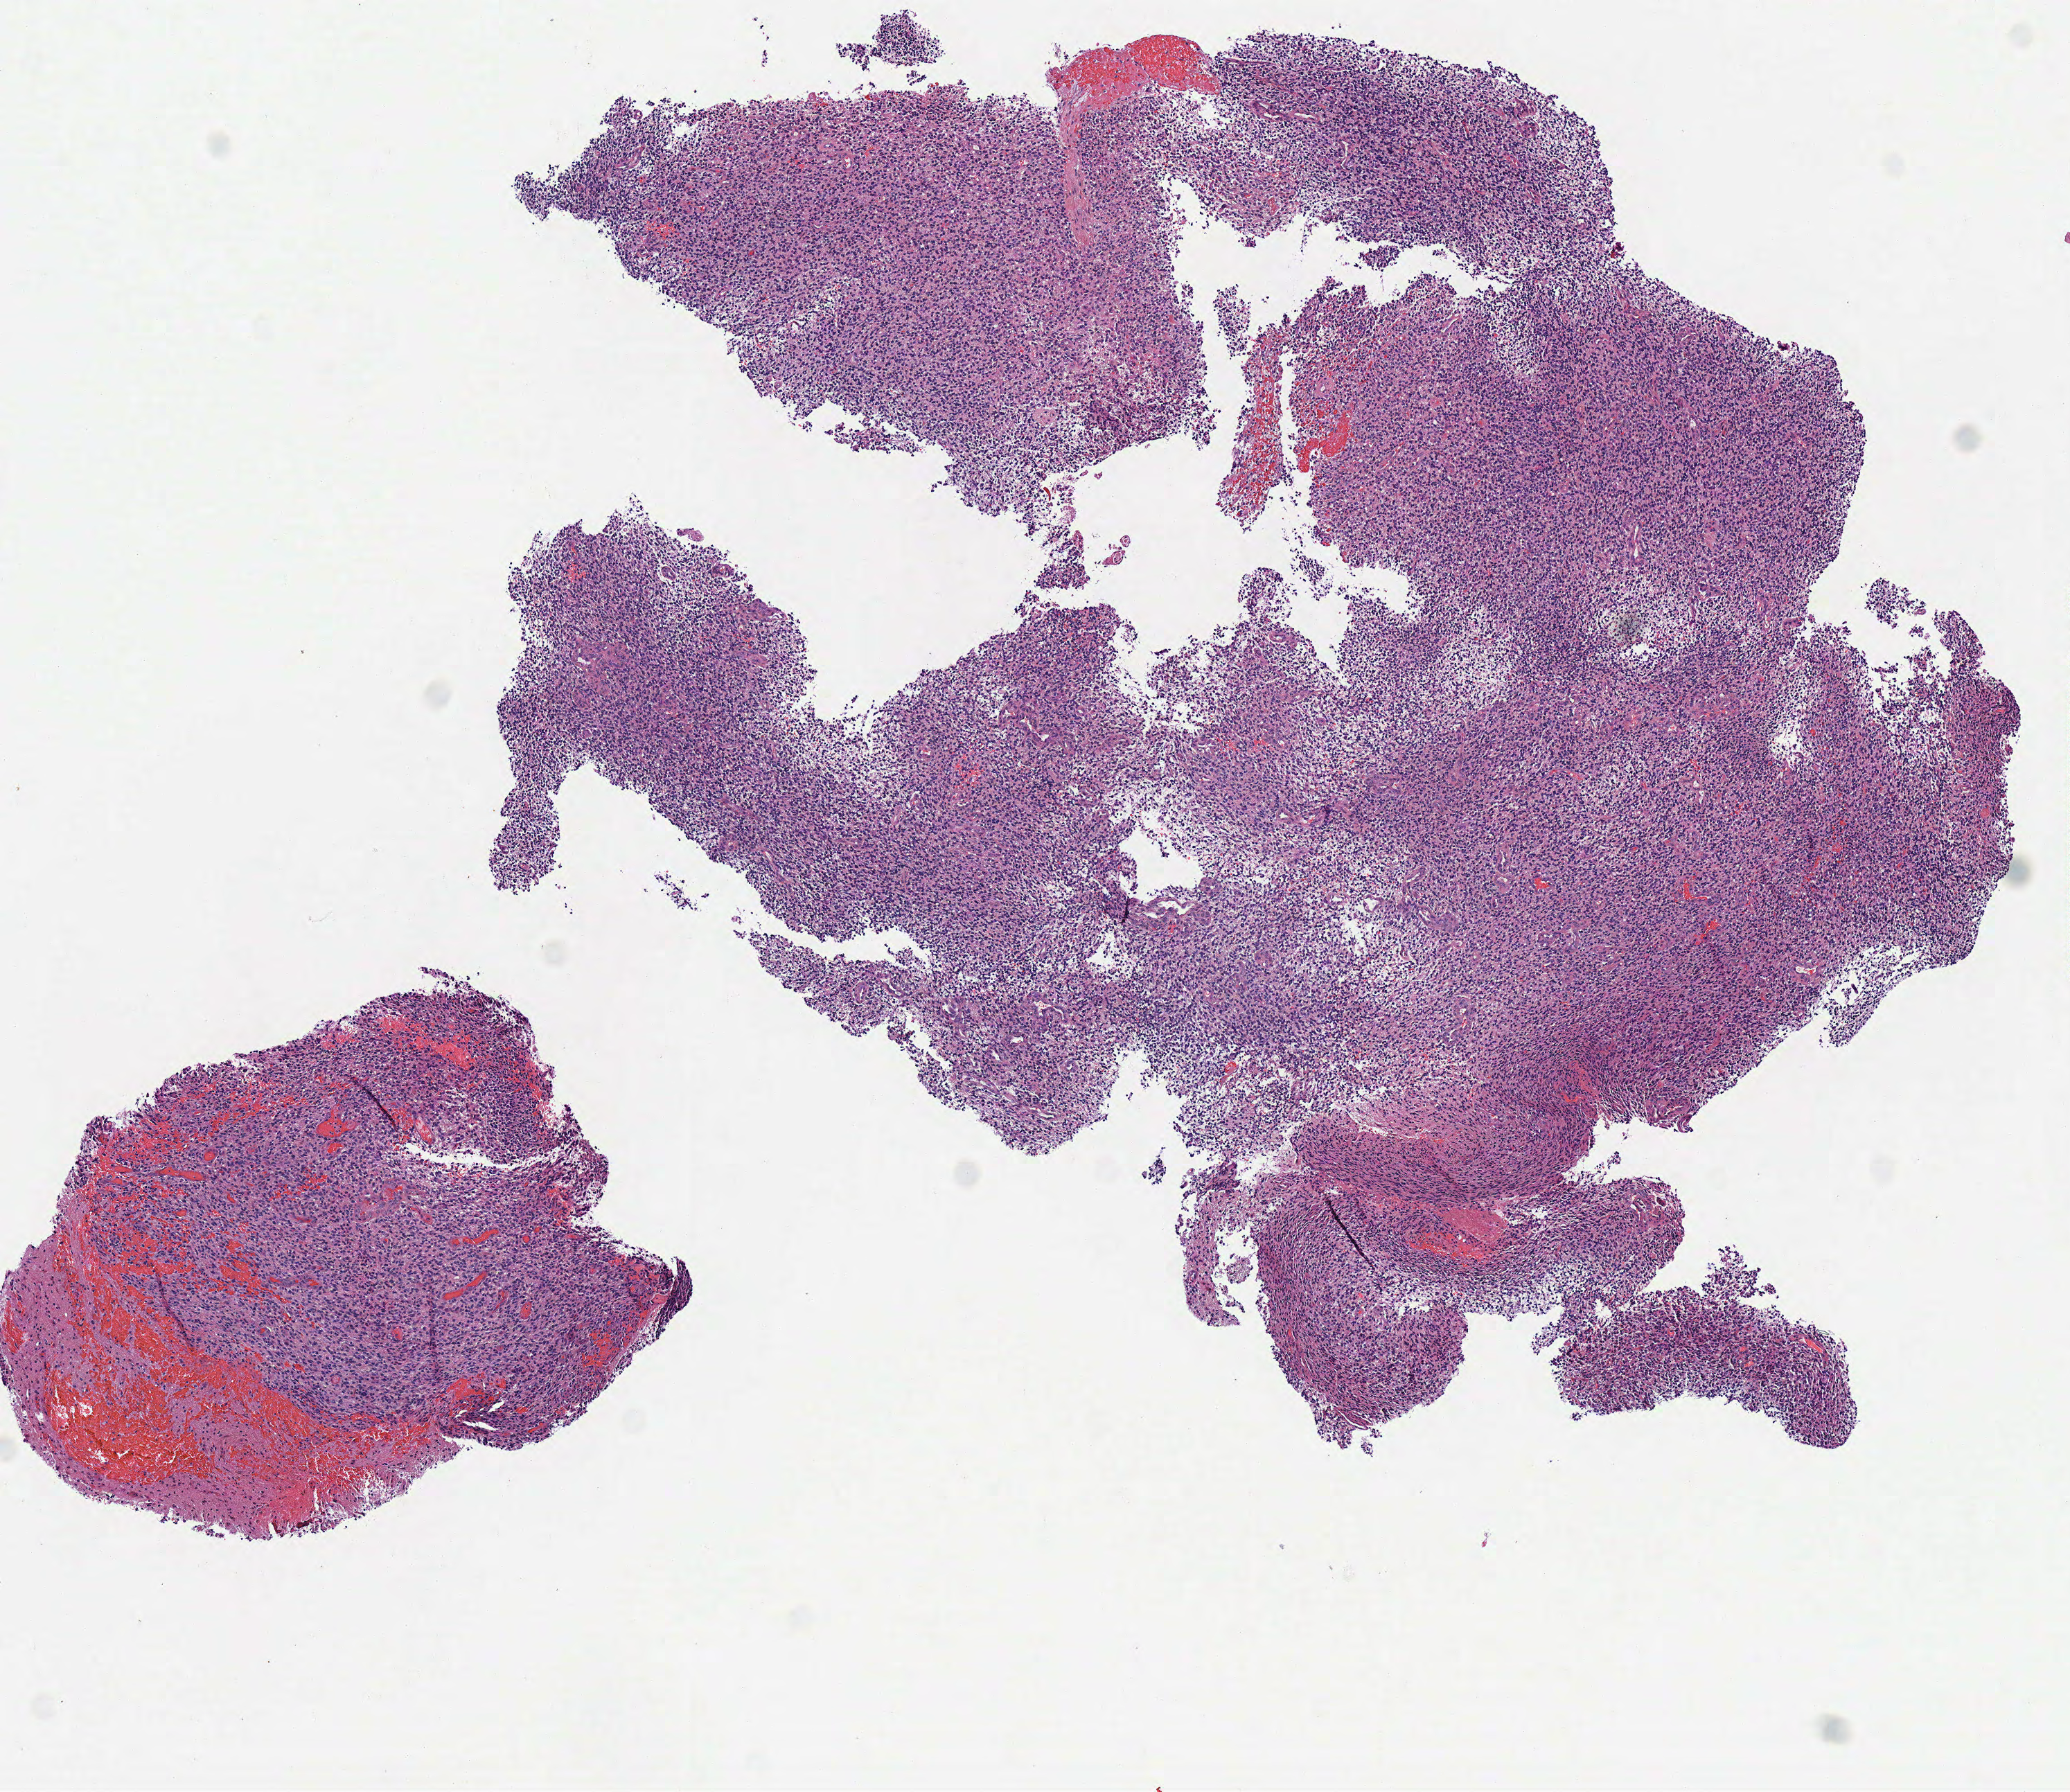
Digitized H&E tissue section (whole slide), whole scanned area (about 5.9 x 5.1 mm, from a 40x scan) shown as a low-resolution overview; frozen section; sample: primary tumour, brain. Female patient; age at initial diagnosis 58 years. Pathologist review of this section (percent, as recorded): tumour cells 100%, tumour nuclei 85%, normal cells 0%, stromal cells 0%, necrosis 0%.
Diagnosis: Glioblastoma.